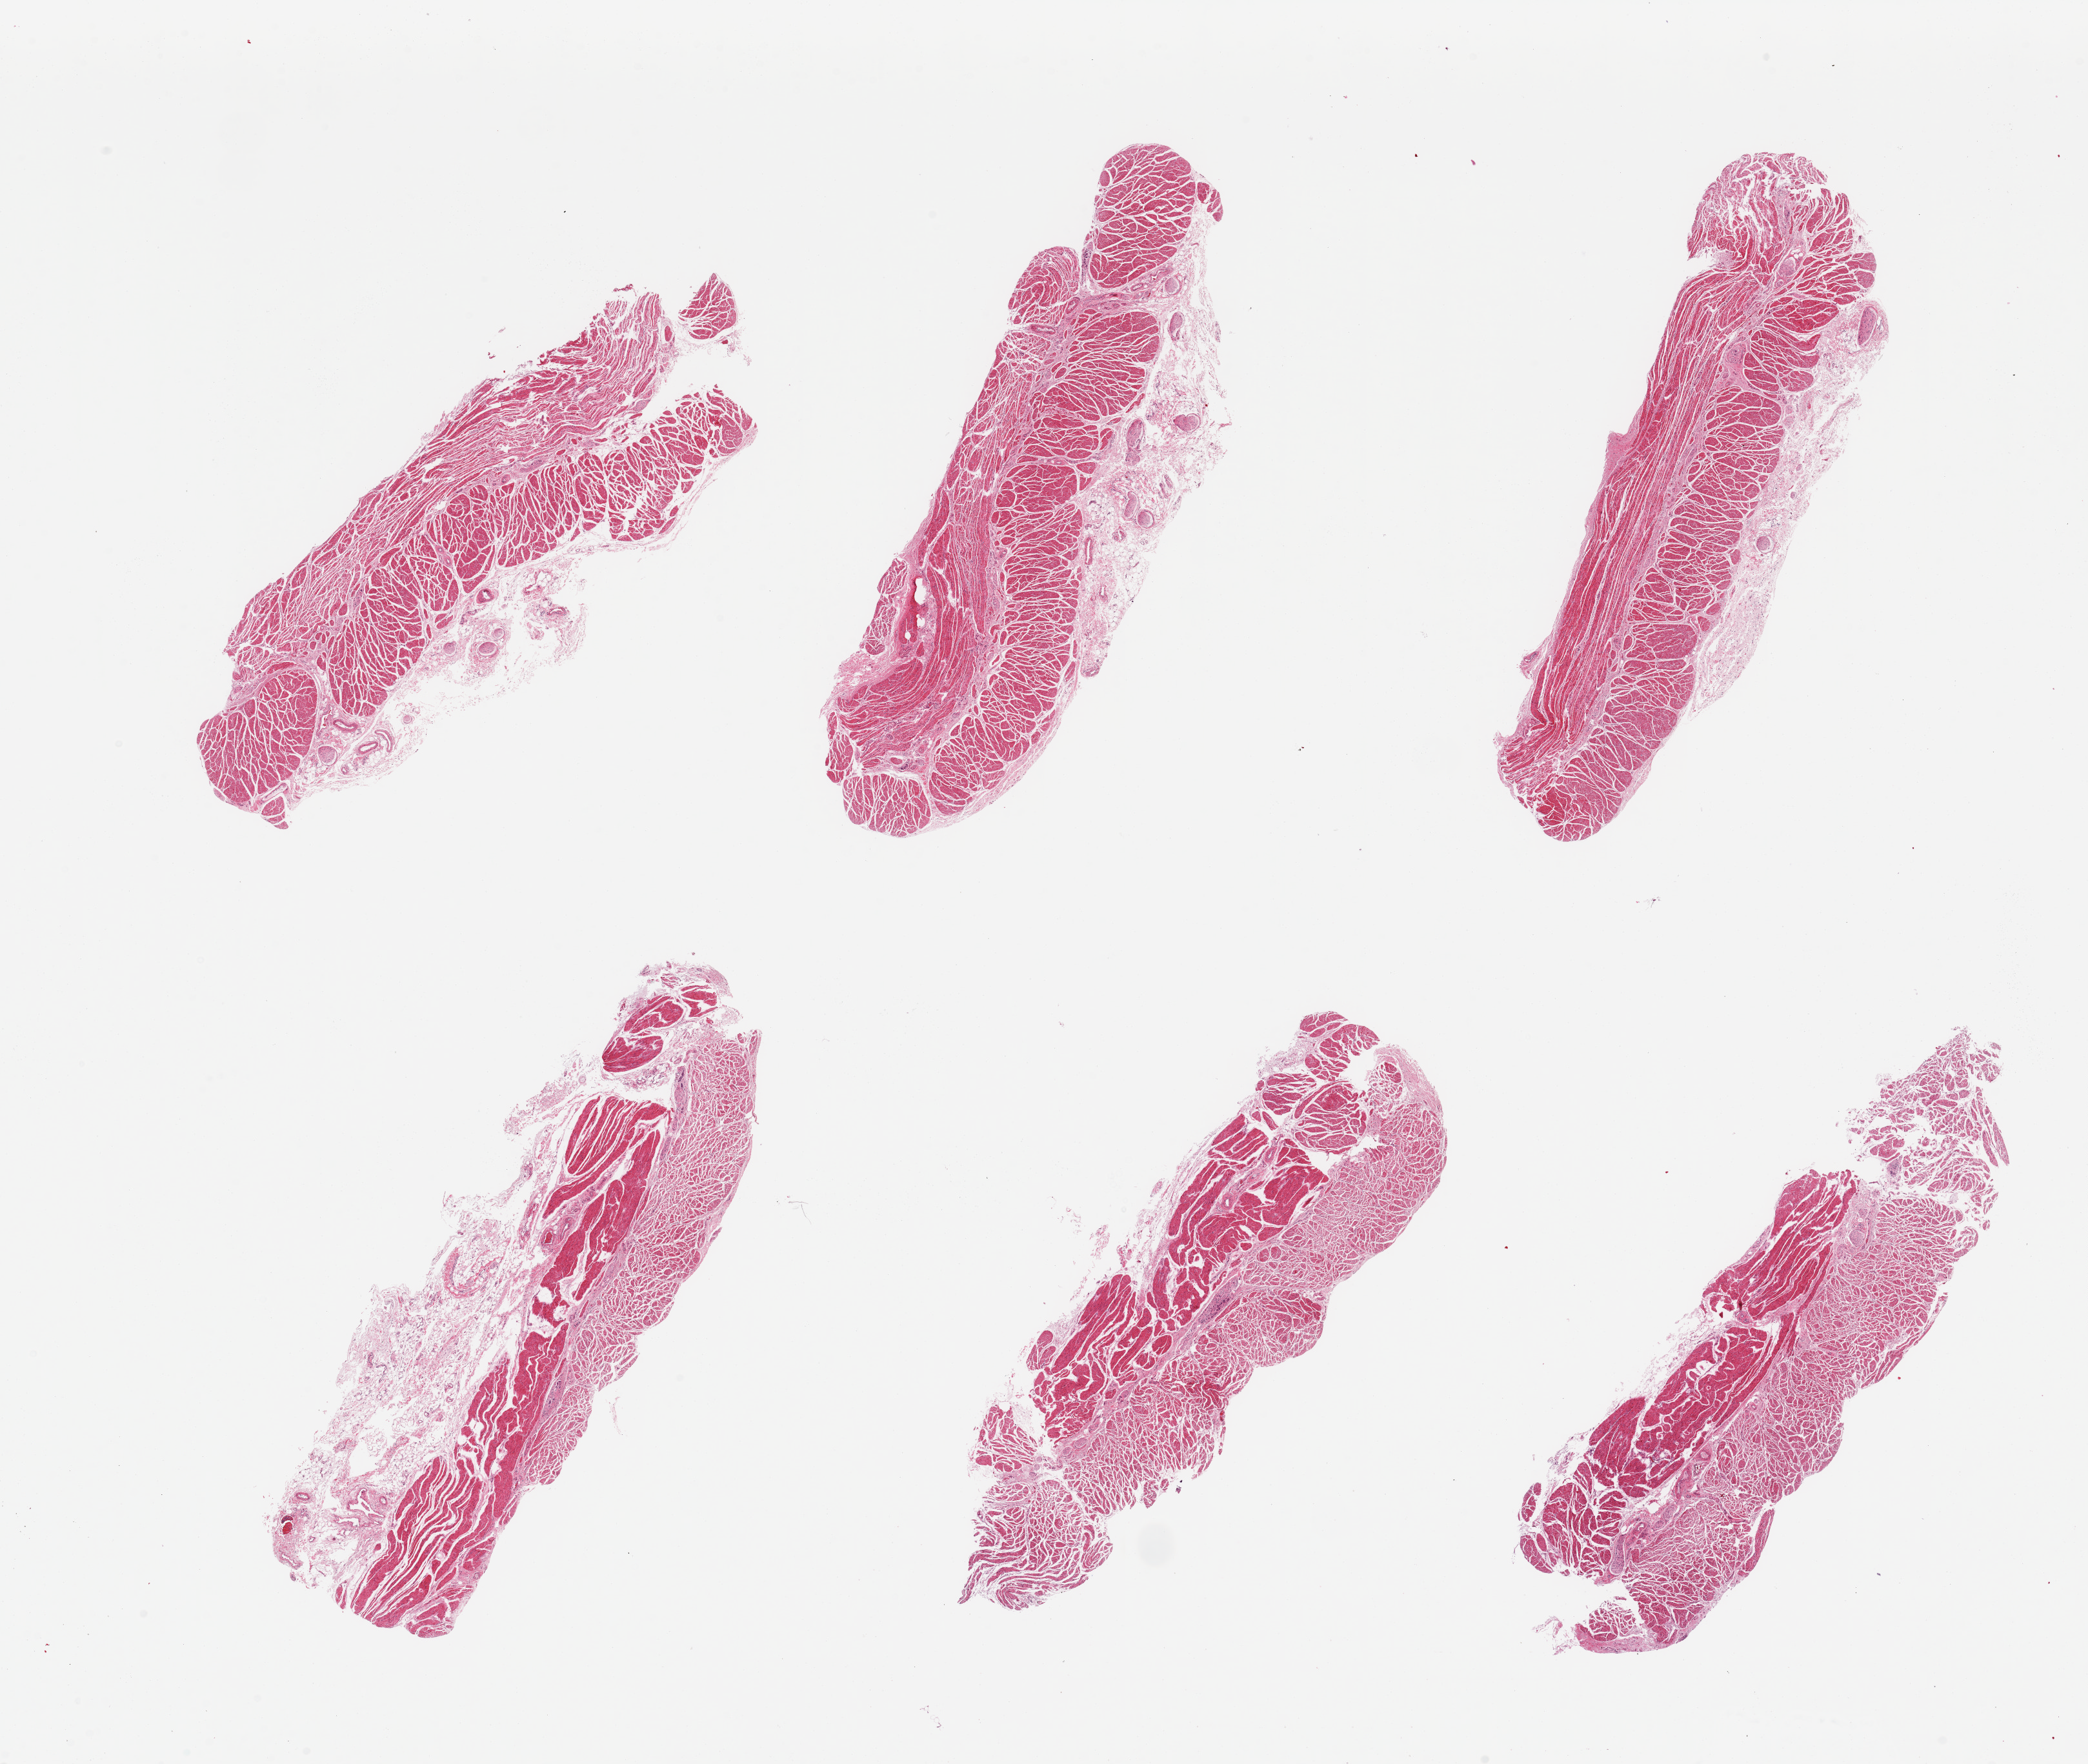
Digitized hematoxylin and eosin (H&E)-stained section, brightfield — a low-resolution overview of the entire scanned area, about 25.6 x 21.6 mm. PAXgene-fixed, paraffin-embedded tissue. Sampled site (target tissue): esophageal muscle. Tissue donor sample.
Reviewer comment on this tissue sample: 6 pieces, confirmed target muscularis6.